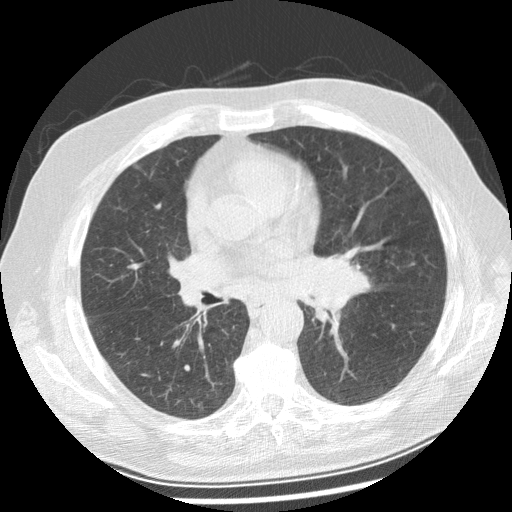
Axial slice from a low-dose chest CT screening exam; first (baseline) screen; lung window (W 1500 / L -600 HU); 2.5 mm slice thickness; 120 kVp. Male, age 70 years at enrolment.
Lesion marked by an expert reader, bounding box (x1, y1, x2, y2) in pixels: (288, 241, 371, 319). Screening reader's record for this exam: no non-calcified nodule ≥4 mm recorded. Official screen result: positive, change unspecified: nodule(s) >= 4 mm or enlarging nodule(s), mass(es), or other non-specific abnormalities suspicious for lung cancer. Participant outcome: lung cancer diagnosed 29 days after this screen — squamous cell carcinoma, keratinizing, NOS, left main stem bronchus, moderately differentiated (G2), stage IIIB (AJCC 6th edition), 40 mm at pathology.